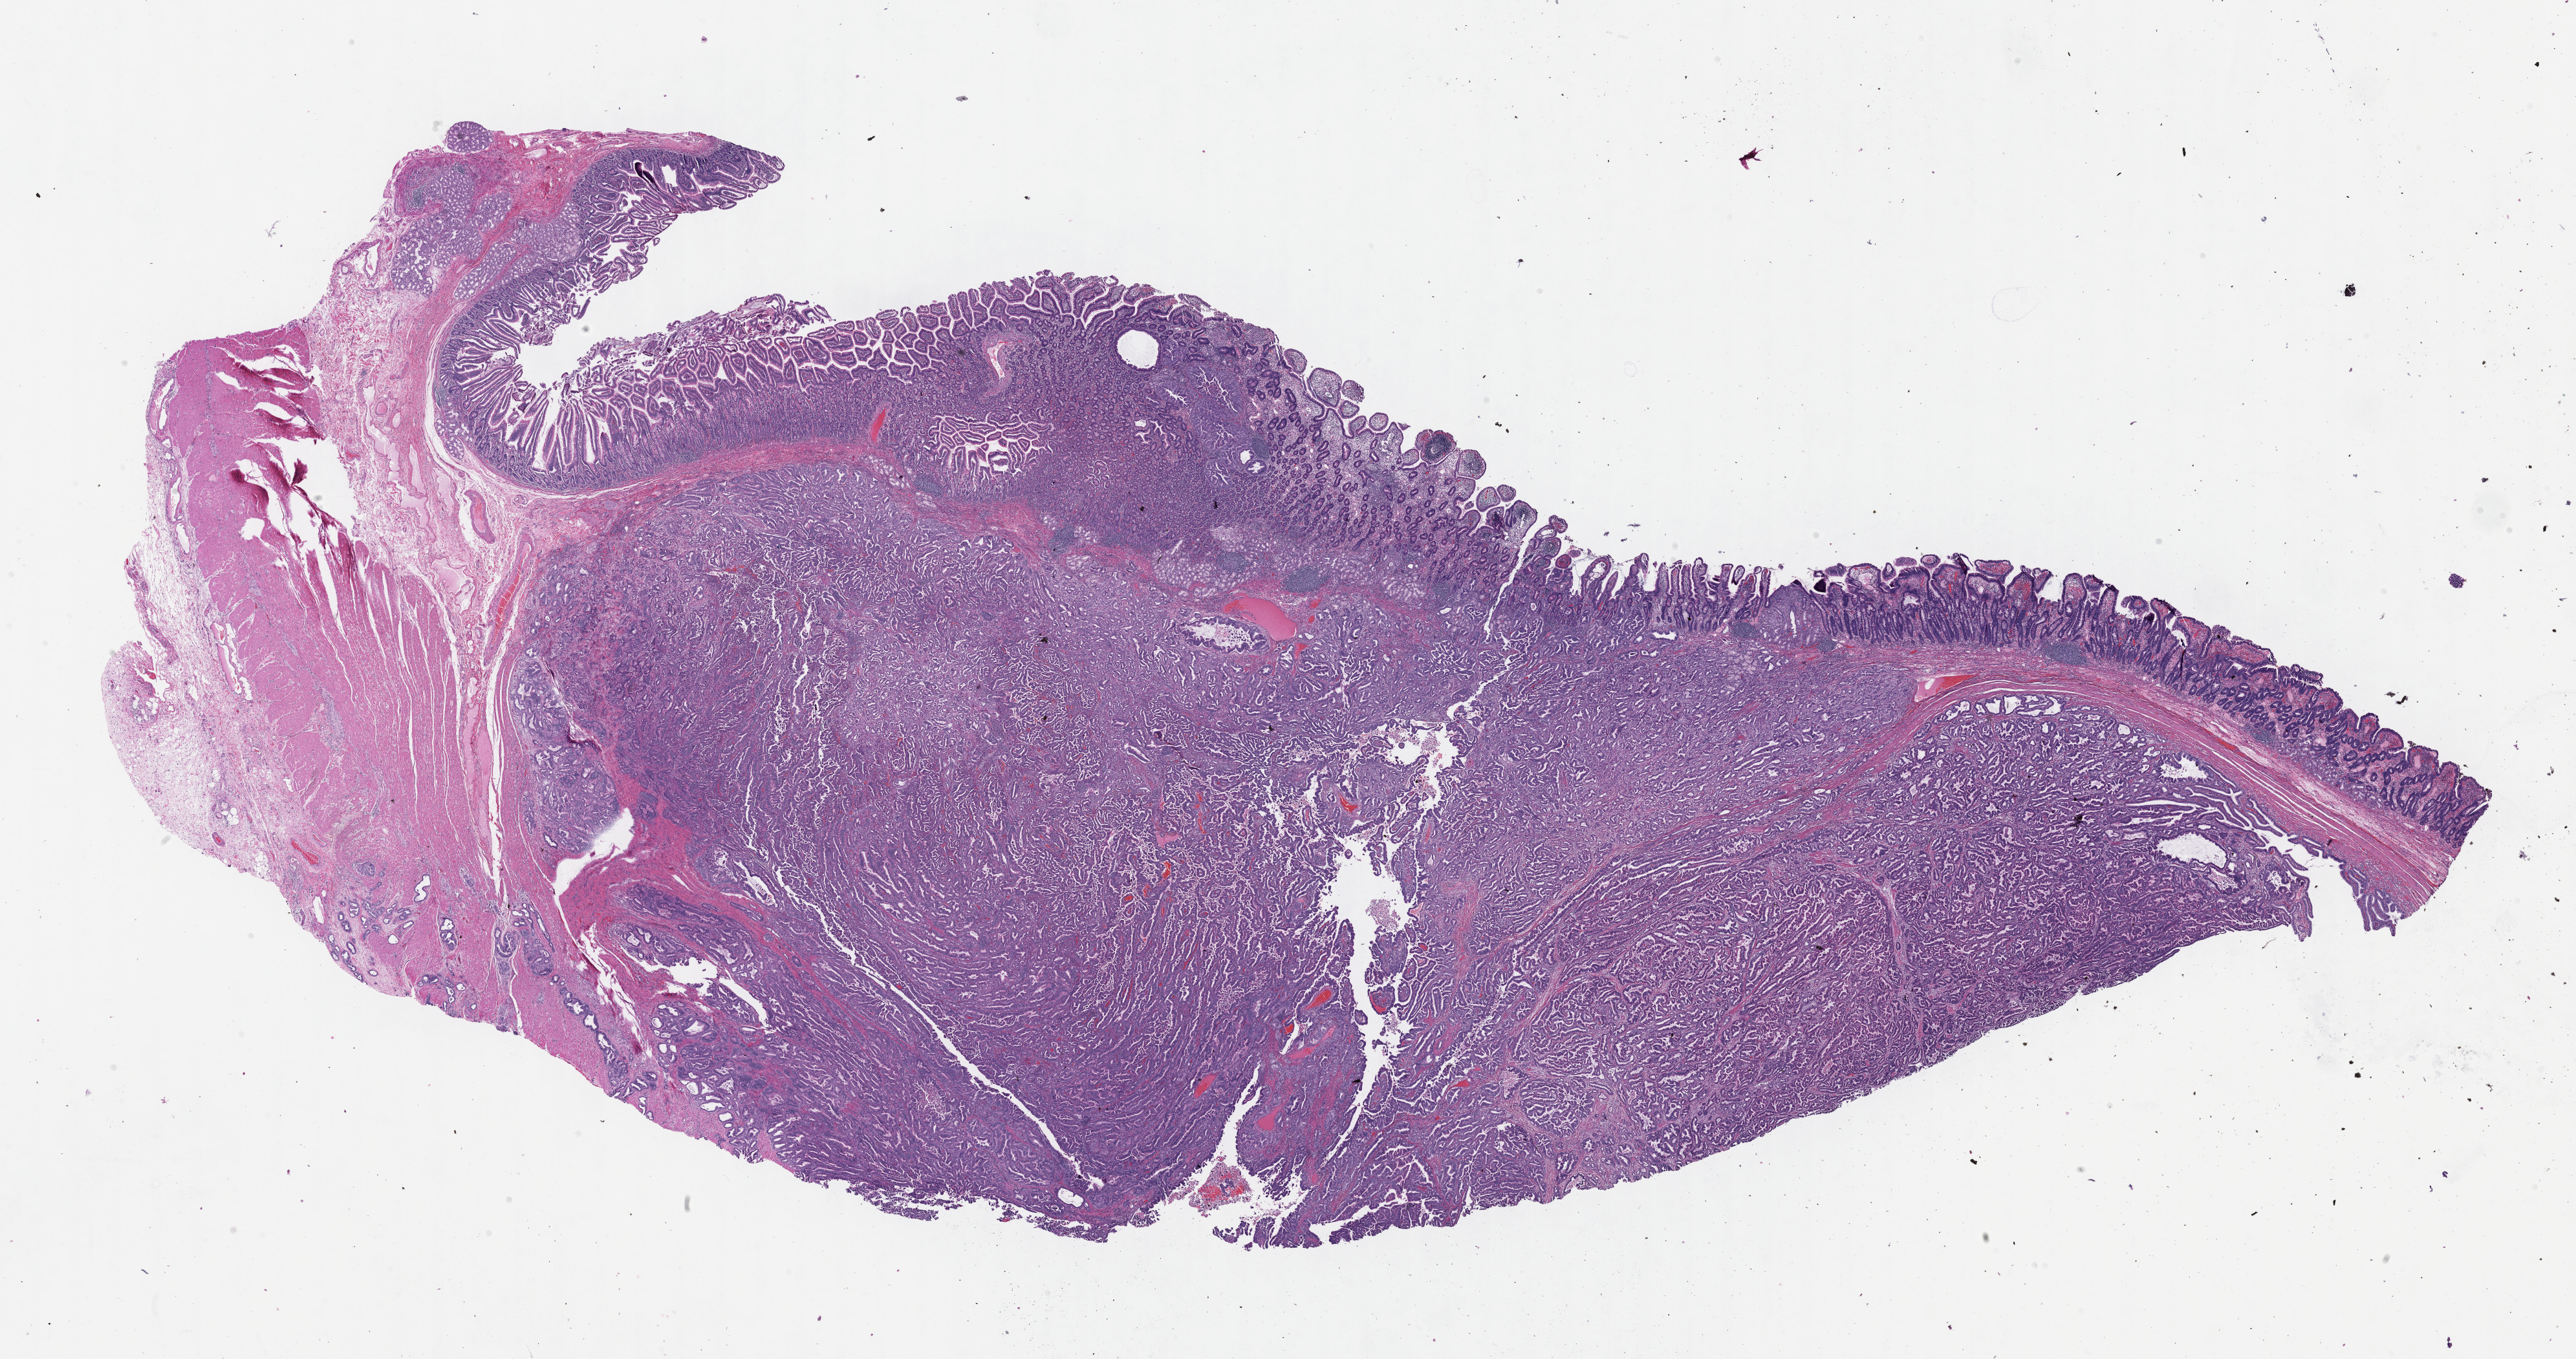
Digitized H&E tissue section (whole slide) — whole scanned area (about 32.2 x 17.0 mm, slide scanned at 40x) shown as a low-resolution overview, formalin-fixed paraffin-embedded (FFPE) diagnostic section, sample: primary tumour, pancreas. Female, age 64 years at initial diagnosis. Histologic grade: G1 (well differentiated).
Histologic diagnosis: Infiltrating duct carcinoma, NOS (head of pancreas). Lymph nodes positive (case pathology): 0 of 10 examined. AJCC pathologic stage: IIA. TNM: T3 N0 MX.